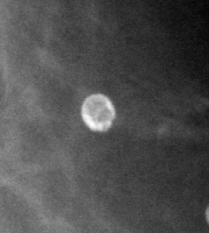
Region of interest cut from a scanned film mammogram (one marked finding); left breast; MLO view; BI-RADS breast density category 3 (scale 1–4).
- Finding: calcifications, morphology round and regular / eggshell; BI-RADS assessment category 2; benign; no additional work-up was recommended (benign without callback).